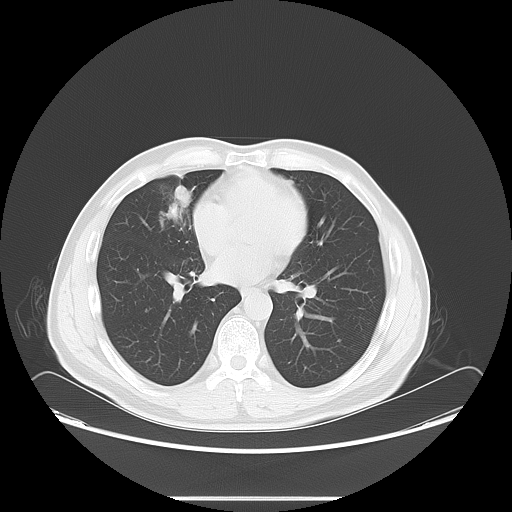
Chest CT, one axial slice; position 36 of 73 along the scan axis; reconstruction kernel LUNG; 120 kVp; lung window (W 1500 / L -600 HU); 5 mm slice thickness; 512 × 512 image matrix, field of view 429 × 429 mm. Male patient, age 47 years. Case-level facts recorded for this patient, not image findings: clinical TNM (as recorded): T1c N3 M0.
Annotated regions visible in this slice (rectangle marked by the reading radiologist):
- lung tumour (recorded histology: adenocarcinoma): bounding box [x1, y1, x2, y2] px = [156, 178, 195, 230]